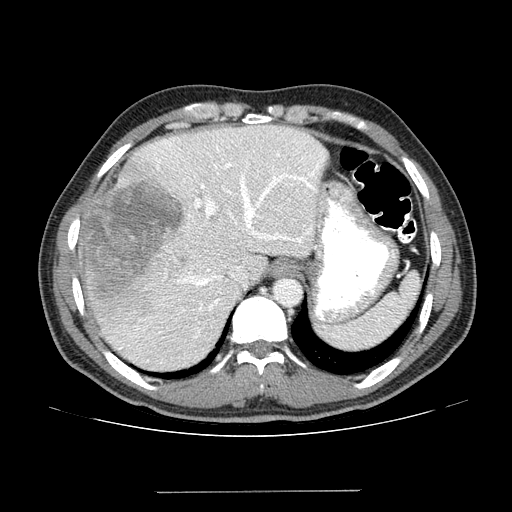
Contrast-enhanced abdominal CT (liver protocol), one axial slice; slice 104 of 131 in the series (ordered by position); 100 kVp; one of 2 acquisitions stored at this slice position; soft-tissue window (W 400 / L 40 HU); 2.5 mm slice thickness; 512 × 512 image matrix, field of view 380 × 380 mm. From the clinical record (not read from this slice): diagnosis: hepatocellular carcinoma (patient treated with transarterial chemoembolisation; whether this scan precedes or follows treatment is not stated here); TNM stage (as recorded): Stage-I; Child-Pugh class: A; tumour size: 10.3 cm.
Annotated regions visible in this slice (semi-automatic segmentation, software-assisted and operator-edited):
- abdominal aorta: bounding box [x1, y1, x2, y2] px = [276, 280, 300, 304]
- liver parenchyma outside the tumour (the mass and vessels are separate outlines, so this box may not span the whole liver): [76, 124, 326, 370]
- mass: [83, 176, 183, 314]
- liver vessels: [119, 131, 324, 363]